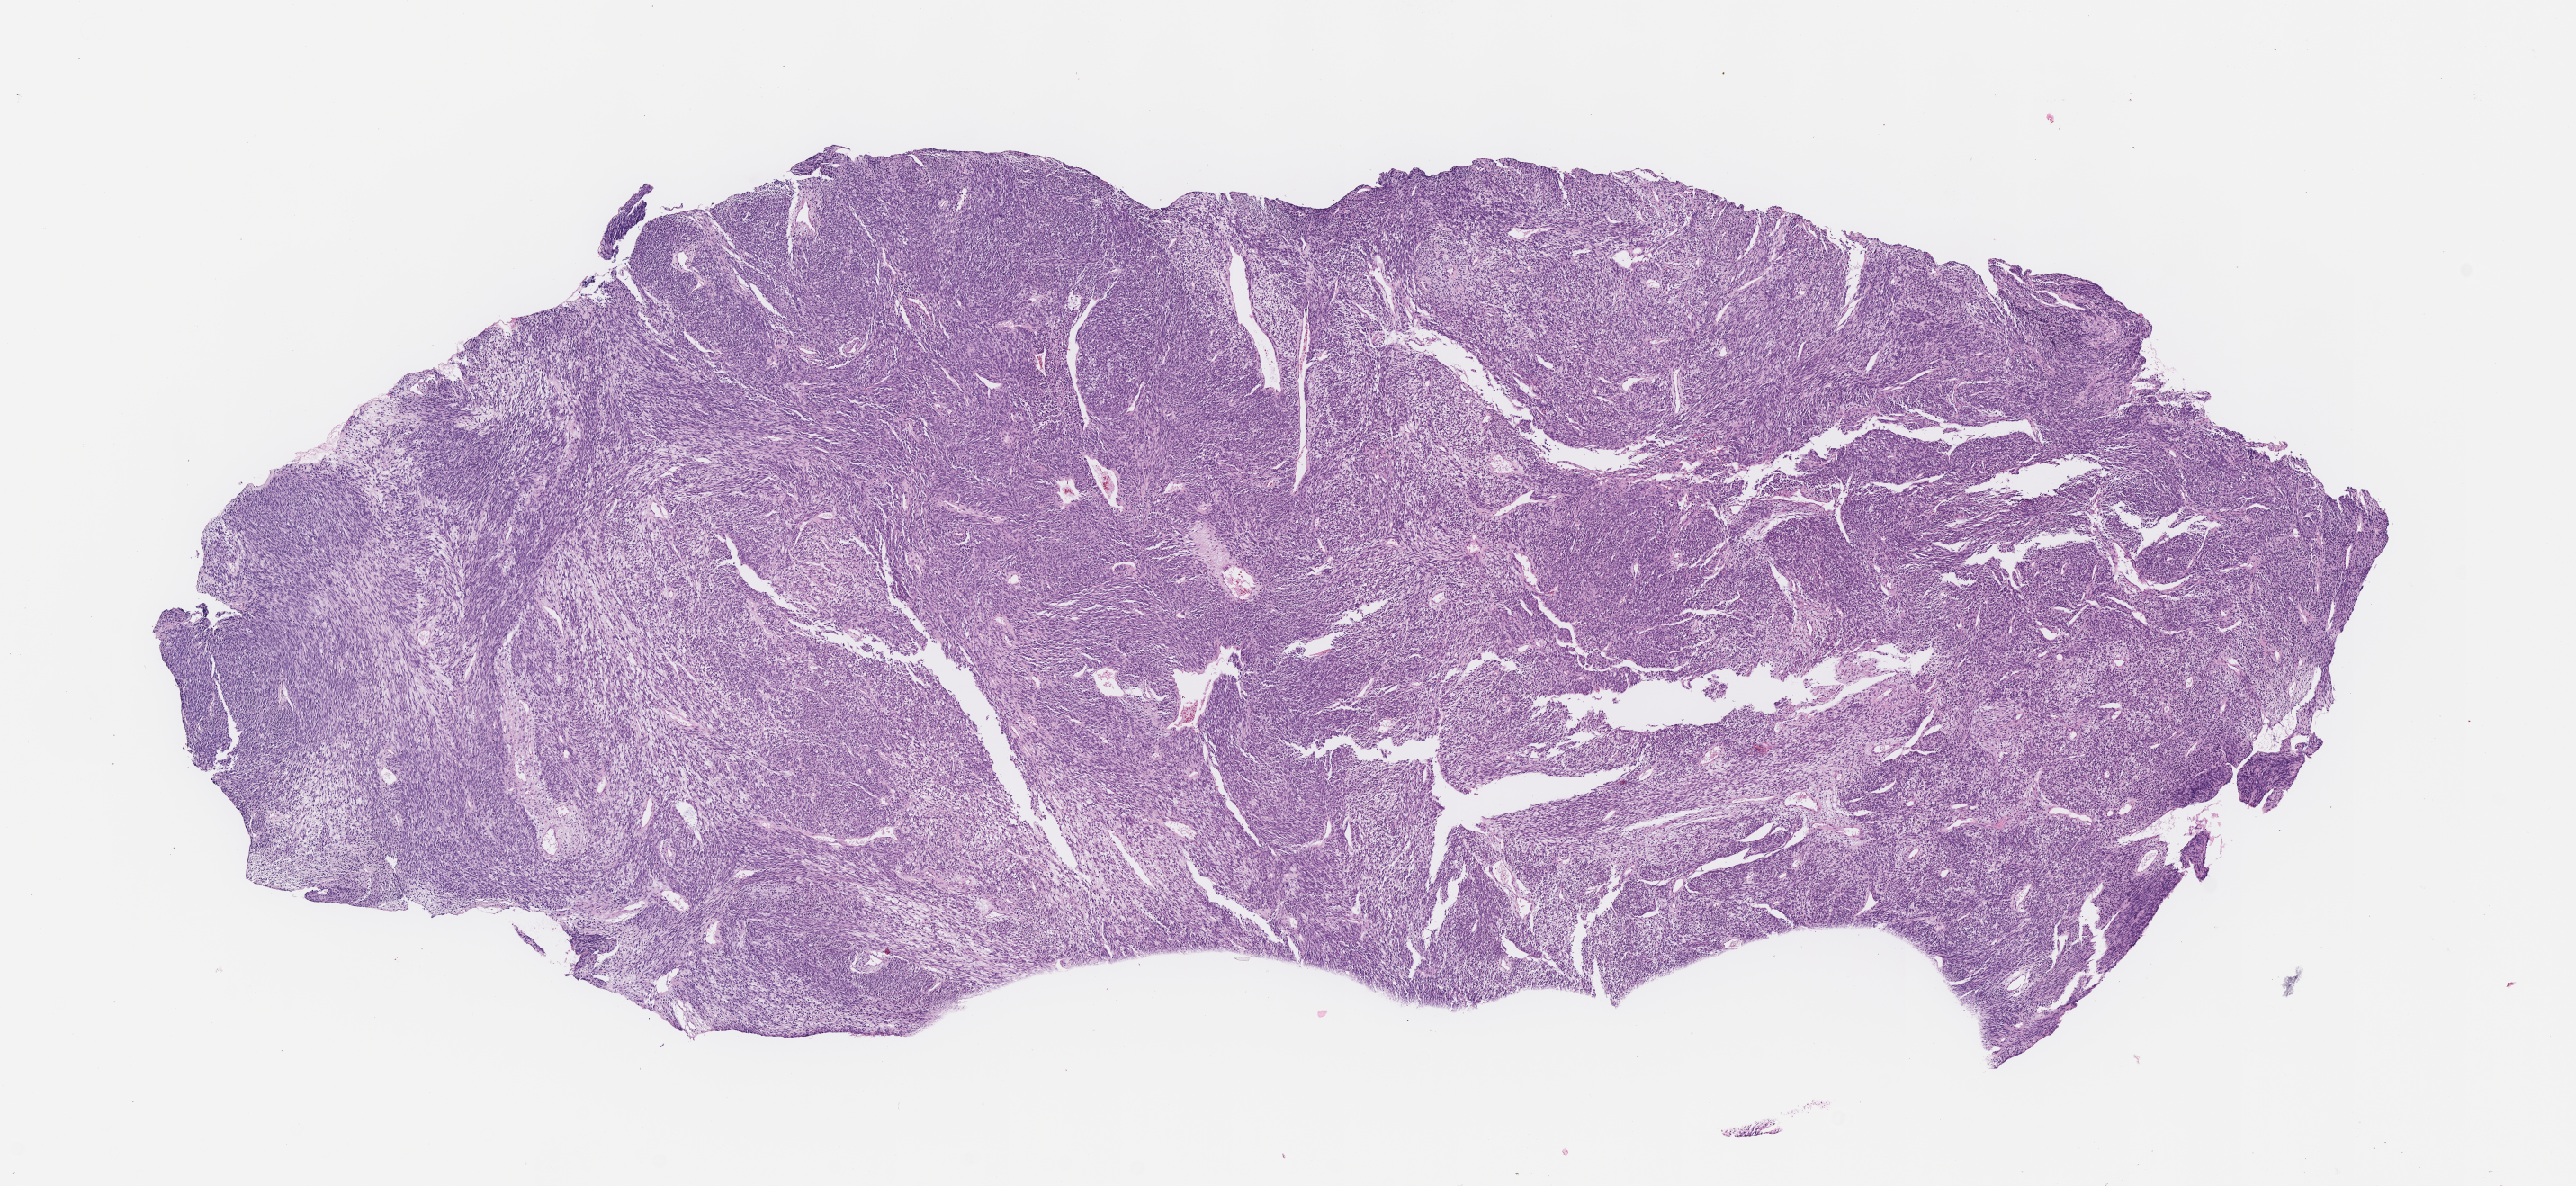
Whole-slide image, haematoxylin and eosin stain of tumor tissue, whole scanned area (about 11.6 x 5.3 mm) shown as a low-resolution overview, formalin-fixed, paraffin-embedded (FFPE) tissue, site: liver. Patient: female, age 3.3 years at diagnosis.
* diagnosis: rhabdomyosarcoma; histological classification: embryonal rhabdomyosarcoma
* stage (as recorded): 3
* metastatic status at presentation (as recorded): non-metastatic (confirmed)